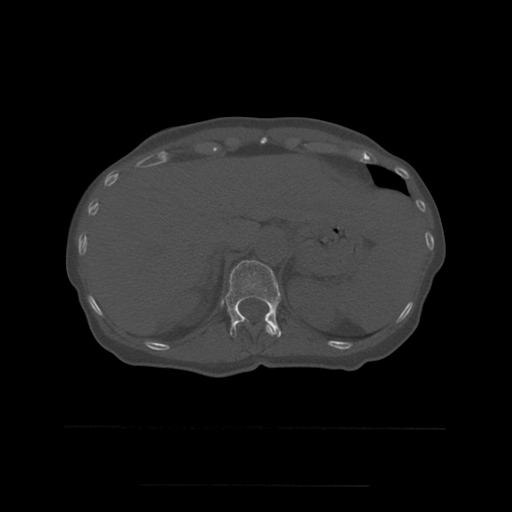
CT including the spine, one axial slice; position 266 of 544 along the scan axis; bone window (W 1800 / L 400 HU); 1.25 mm slice thickness; 512 × 512 image matrix, field of view 350 × 350 mm. Patient age 58 years. From the clinical record (not read from this slice): primary cancer: lung.
Outlined on this slice (semi-automatic segmentation, software-assisted and operator-edited):
- T11 vertebra: bounding box <236,320,278,336> (left, top, right, bottom; pixels)
- T12 vertebra: <223,261,282,338>